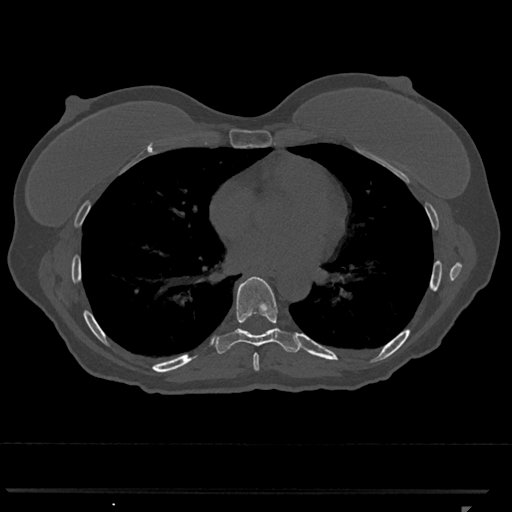
CT including the spine, one axial slice; position 669 of 793 along the scan axis; reconstruction kernel Br40s/3; 120 kVp; bone window (W 1800 / L 400 HU); 512 × 512 image matrix. Female patient, age 62 years. Case-level facts recorded for this patient, not image findings: primary cancer: renal.
Structures marked on this image (semi-automatically segmented with operator editing):
- T7 vertebra: bounding box [x1, y1, x2, y2] px = [253, 353, 259, 371]
- T8 vertebra: [215, 277, 299, 354]